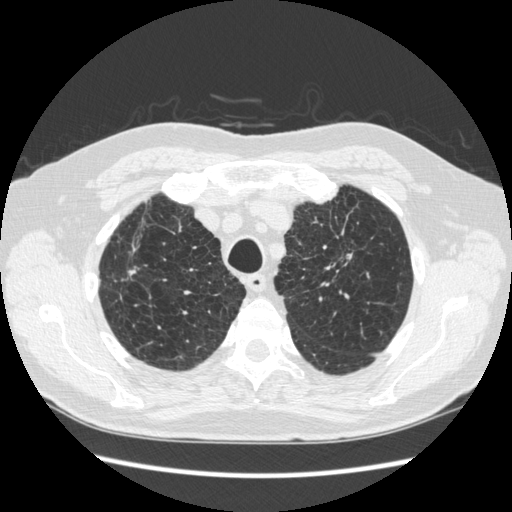
Low-dose screening chest CT, one axial slice; lung window (W 1500 / L -600 HU); 1.25 mm slice thickness; 512 × 512 image matrix.
Structures marked on this image (manually delineated by an expert):
- lesion 1 (tumor, upper lobe of left lung): bounding box [x1, y1, x2, y2] px = [345, 254, 352, 265]